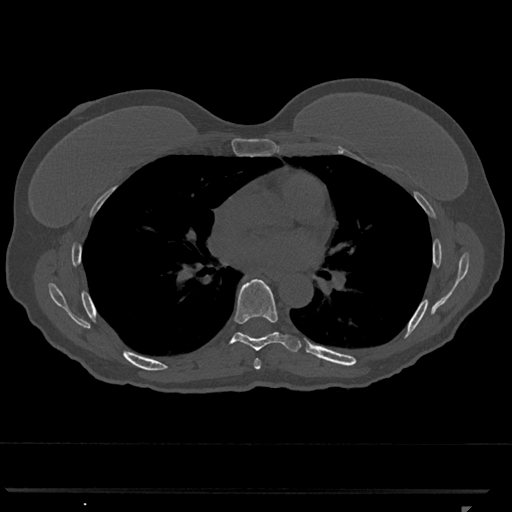
CT including the spine, one axial slice. Position 711 of 793 along the scan axis. Reconstruction kernel Br40s/3. 120 kVp. Bone window (W 1800 / L 400 HU). 0.5 mm slice thickness. 512 × 512 image matrix, field of view 380 × 380 mm. Female patient, age 62 years. Case-level facts recorded for this patient, not image findings: primary cancer: renal.
Annotated regions visible in this slice (semi-automatic segmentation, software-assisted and operator-edited):
- T6 vertebra: box from (x=254, y=359) to (x=261, y=370) px
- T7 vertebra: (x=221, y=279)–(x=301, y=352)